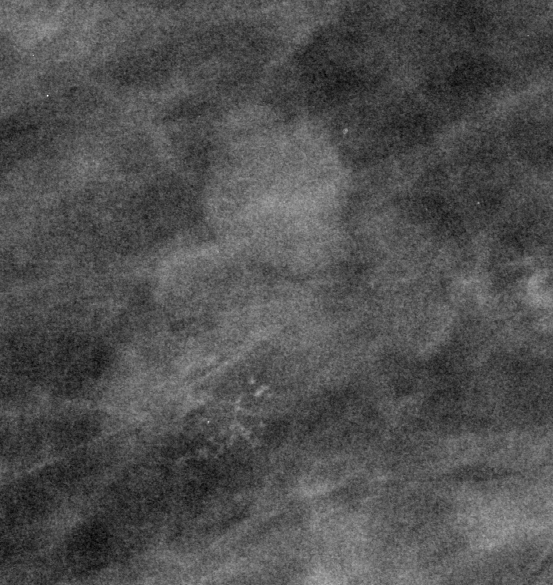
Region of interest cut from a scanned film mammogram (one marked finding); left breast; CC view; BI-RADS breast density category 2 (scale 1–4).
Marked abnormality: calcifications, morphology amorphous, distribution clustered; BI-RADS assessment category 4; subtlety rating 4 on a 1 (subtle) to 5 (obvious) scale; pathology (as recorded): malignant.